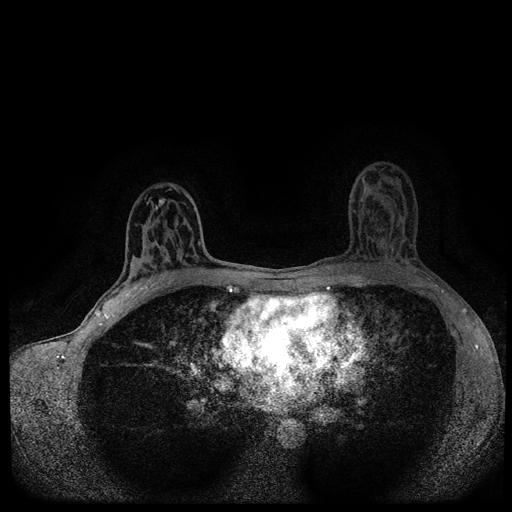
Breast MRI (dynamic contrast-enhanced, multi-phase), one axial slice; slice 58 of 116 in the series (ordered by position); dynamic contrast-enhanced series, time point 2 of 5 at this slice position (early post-contrast); 1.5 T; TE 2.7 ms, TR 5.4 ms; 512 × 512 image matrix, field of view 320 × 320 mm. Patient: female, 43 years.
Annotated regions visible in this slice (semi-automatic segmentation, software-assisted and operator-edited):
- breast lesion (labelled 'tumour' in the annotation; benign lesions carry a separate 'benign' label): bounding box [x1, y1, x2, y2] px = [158, 197, 166, 208]